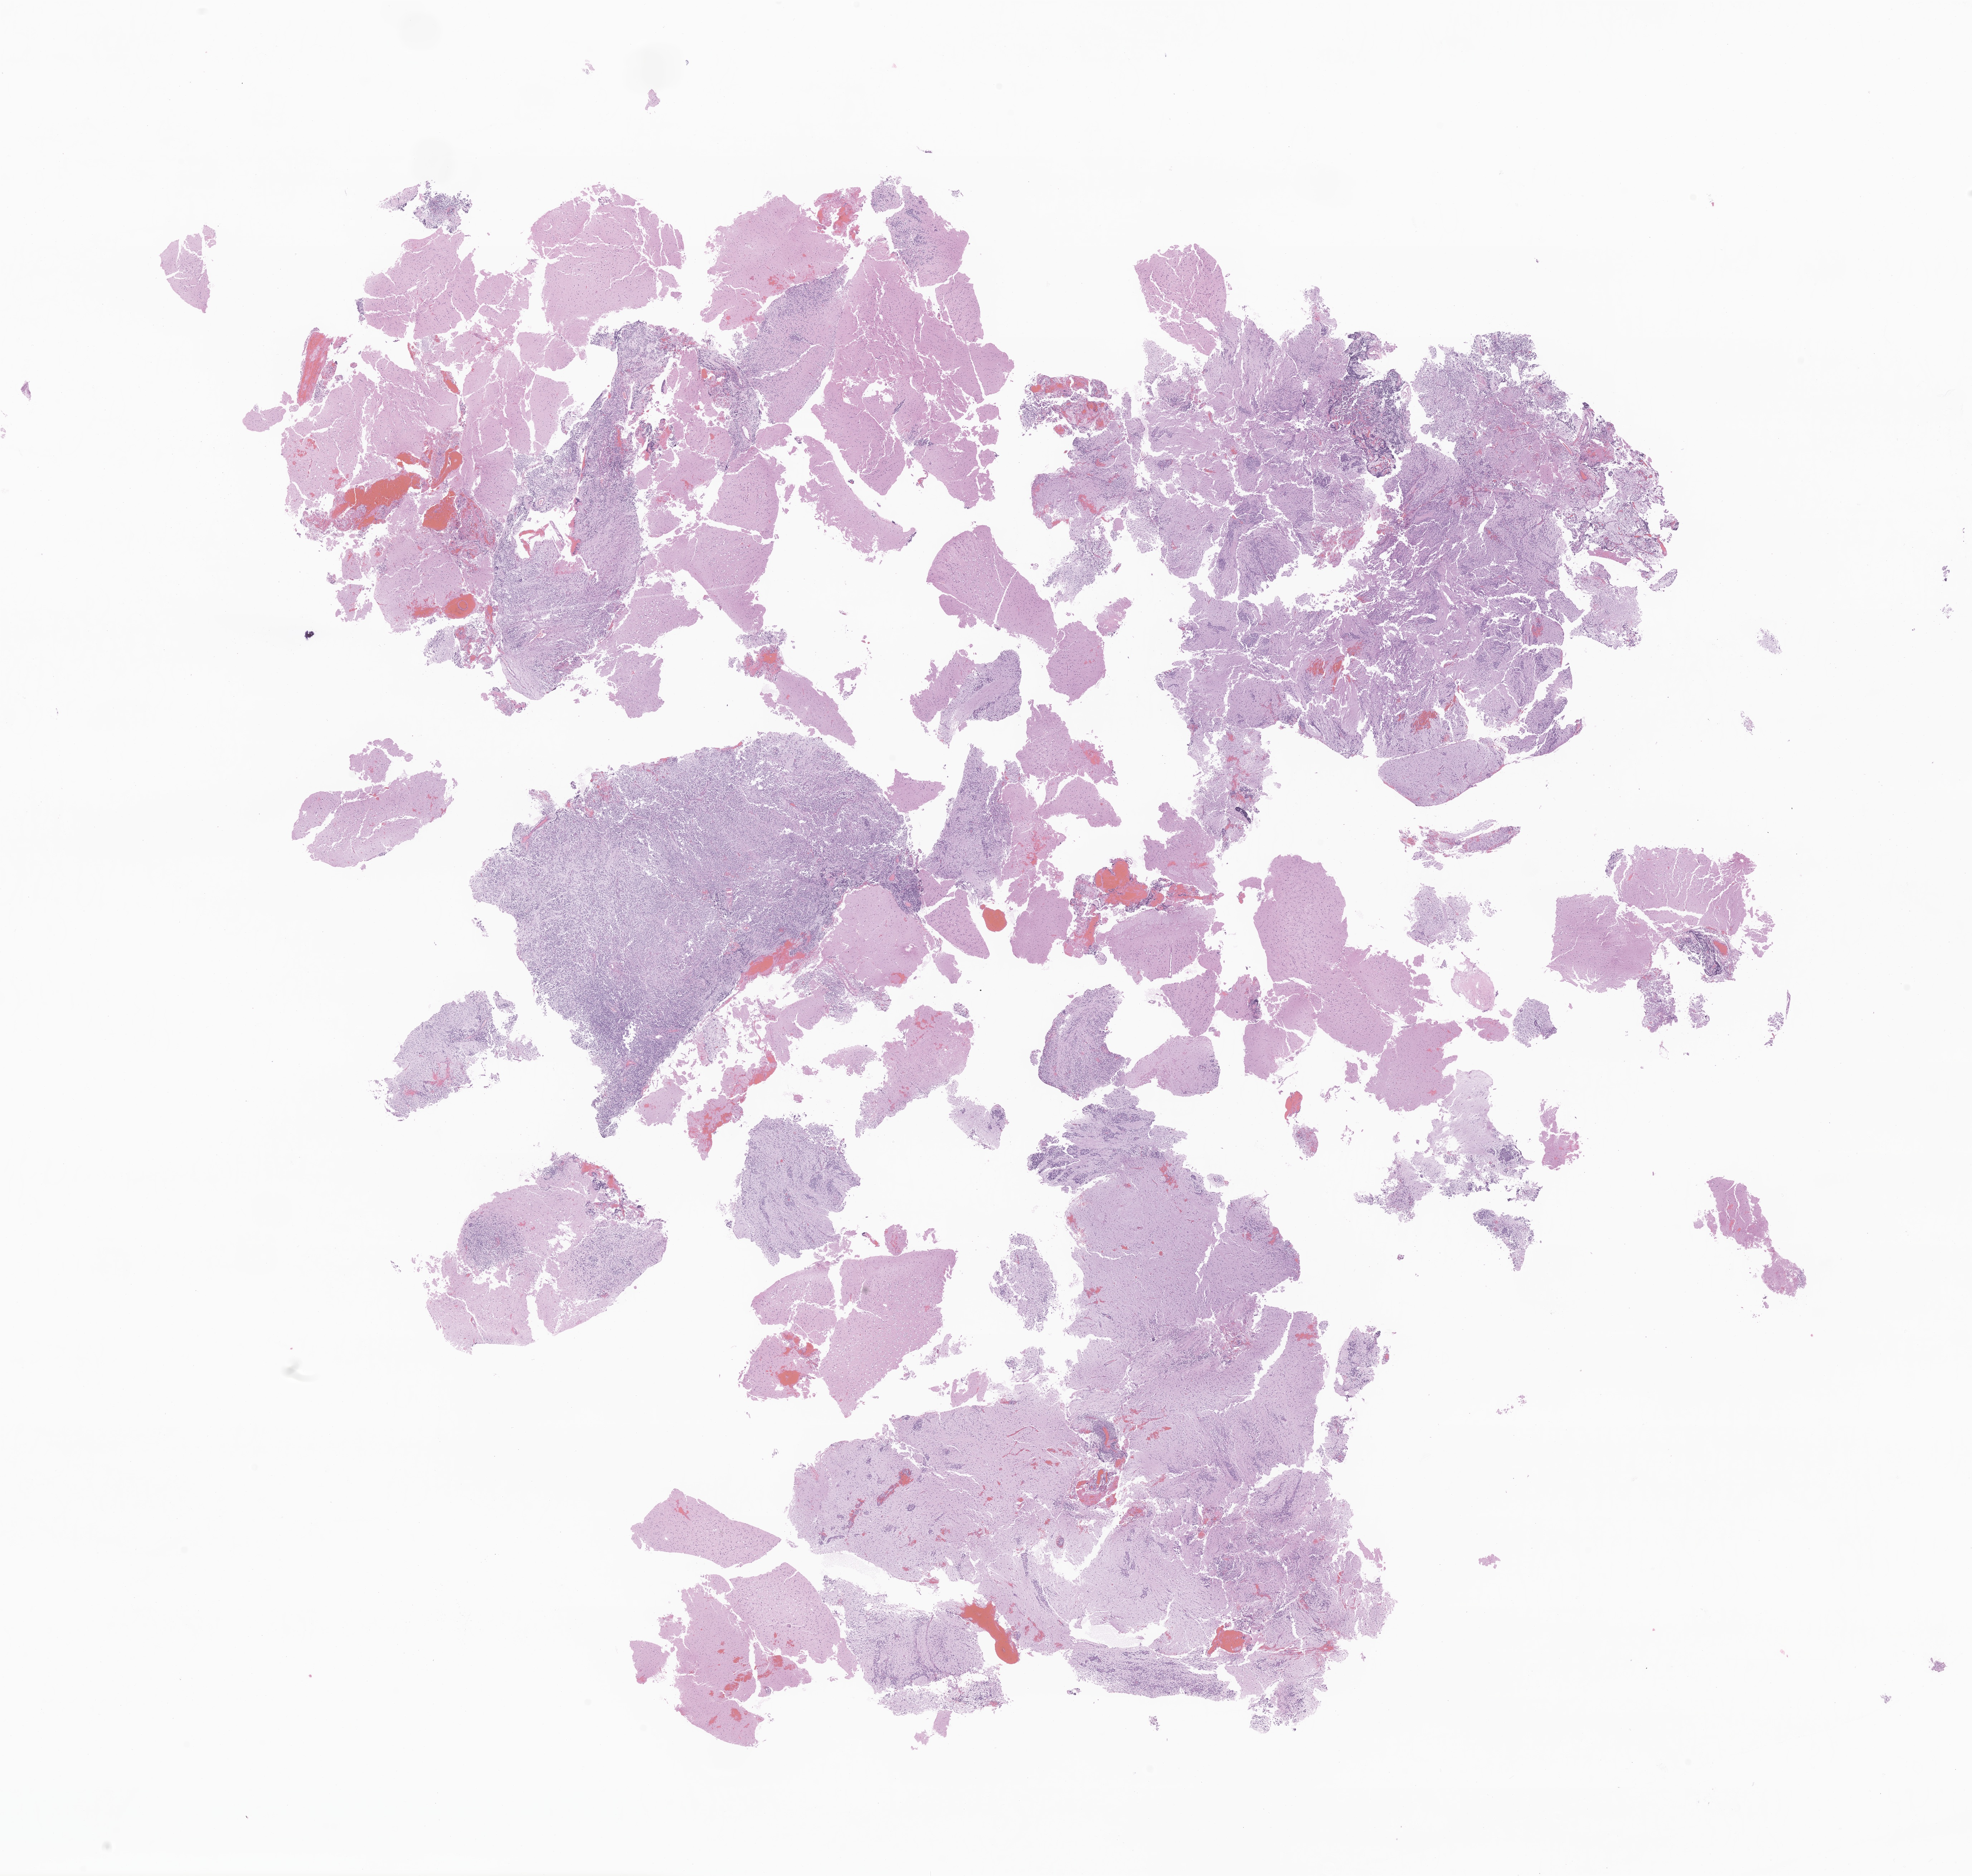
Whole-slide image, haematoxylin and eosin stain of tumor tissue from the brain — shown as a low-resolution overview of the whole scanned area (about 23.2 x 22.1 mm), formalin-fixed, paraffin-embedded (FFPE) tissue. Patient female; age 677 days (about 1.9 years).
Recorded diagnosis: CNS embryonal tumor, NOS.